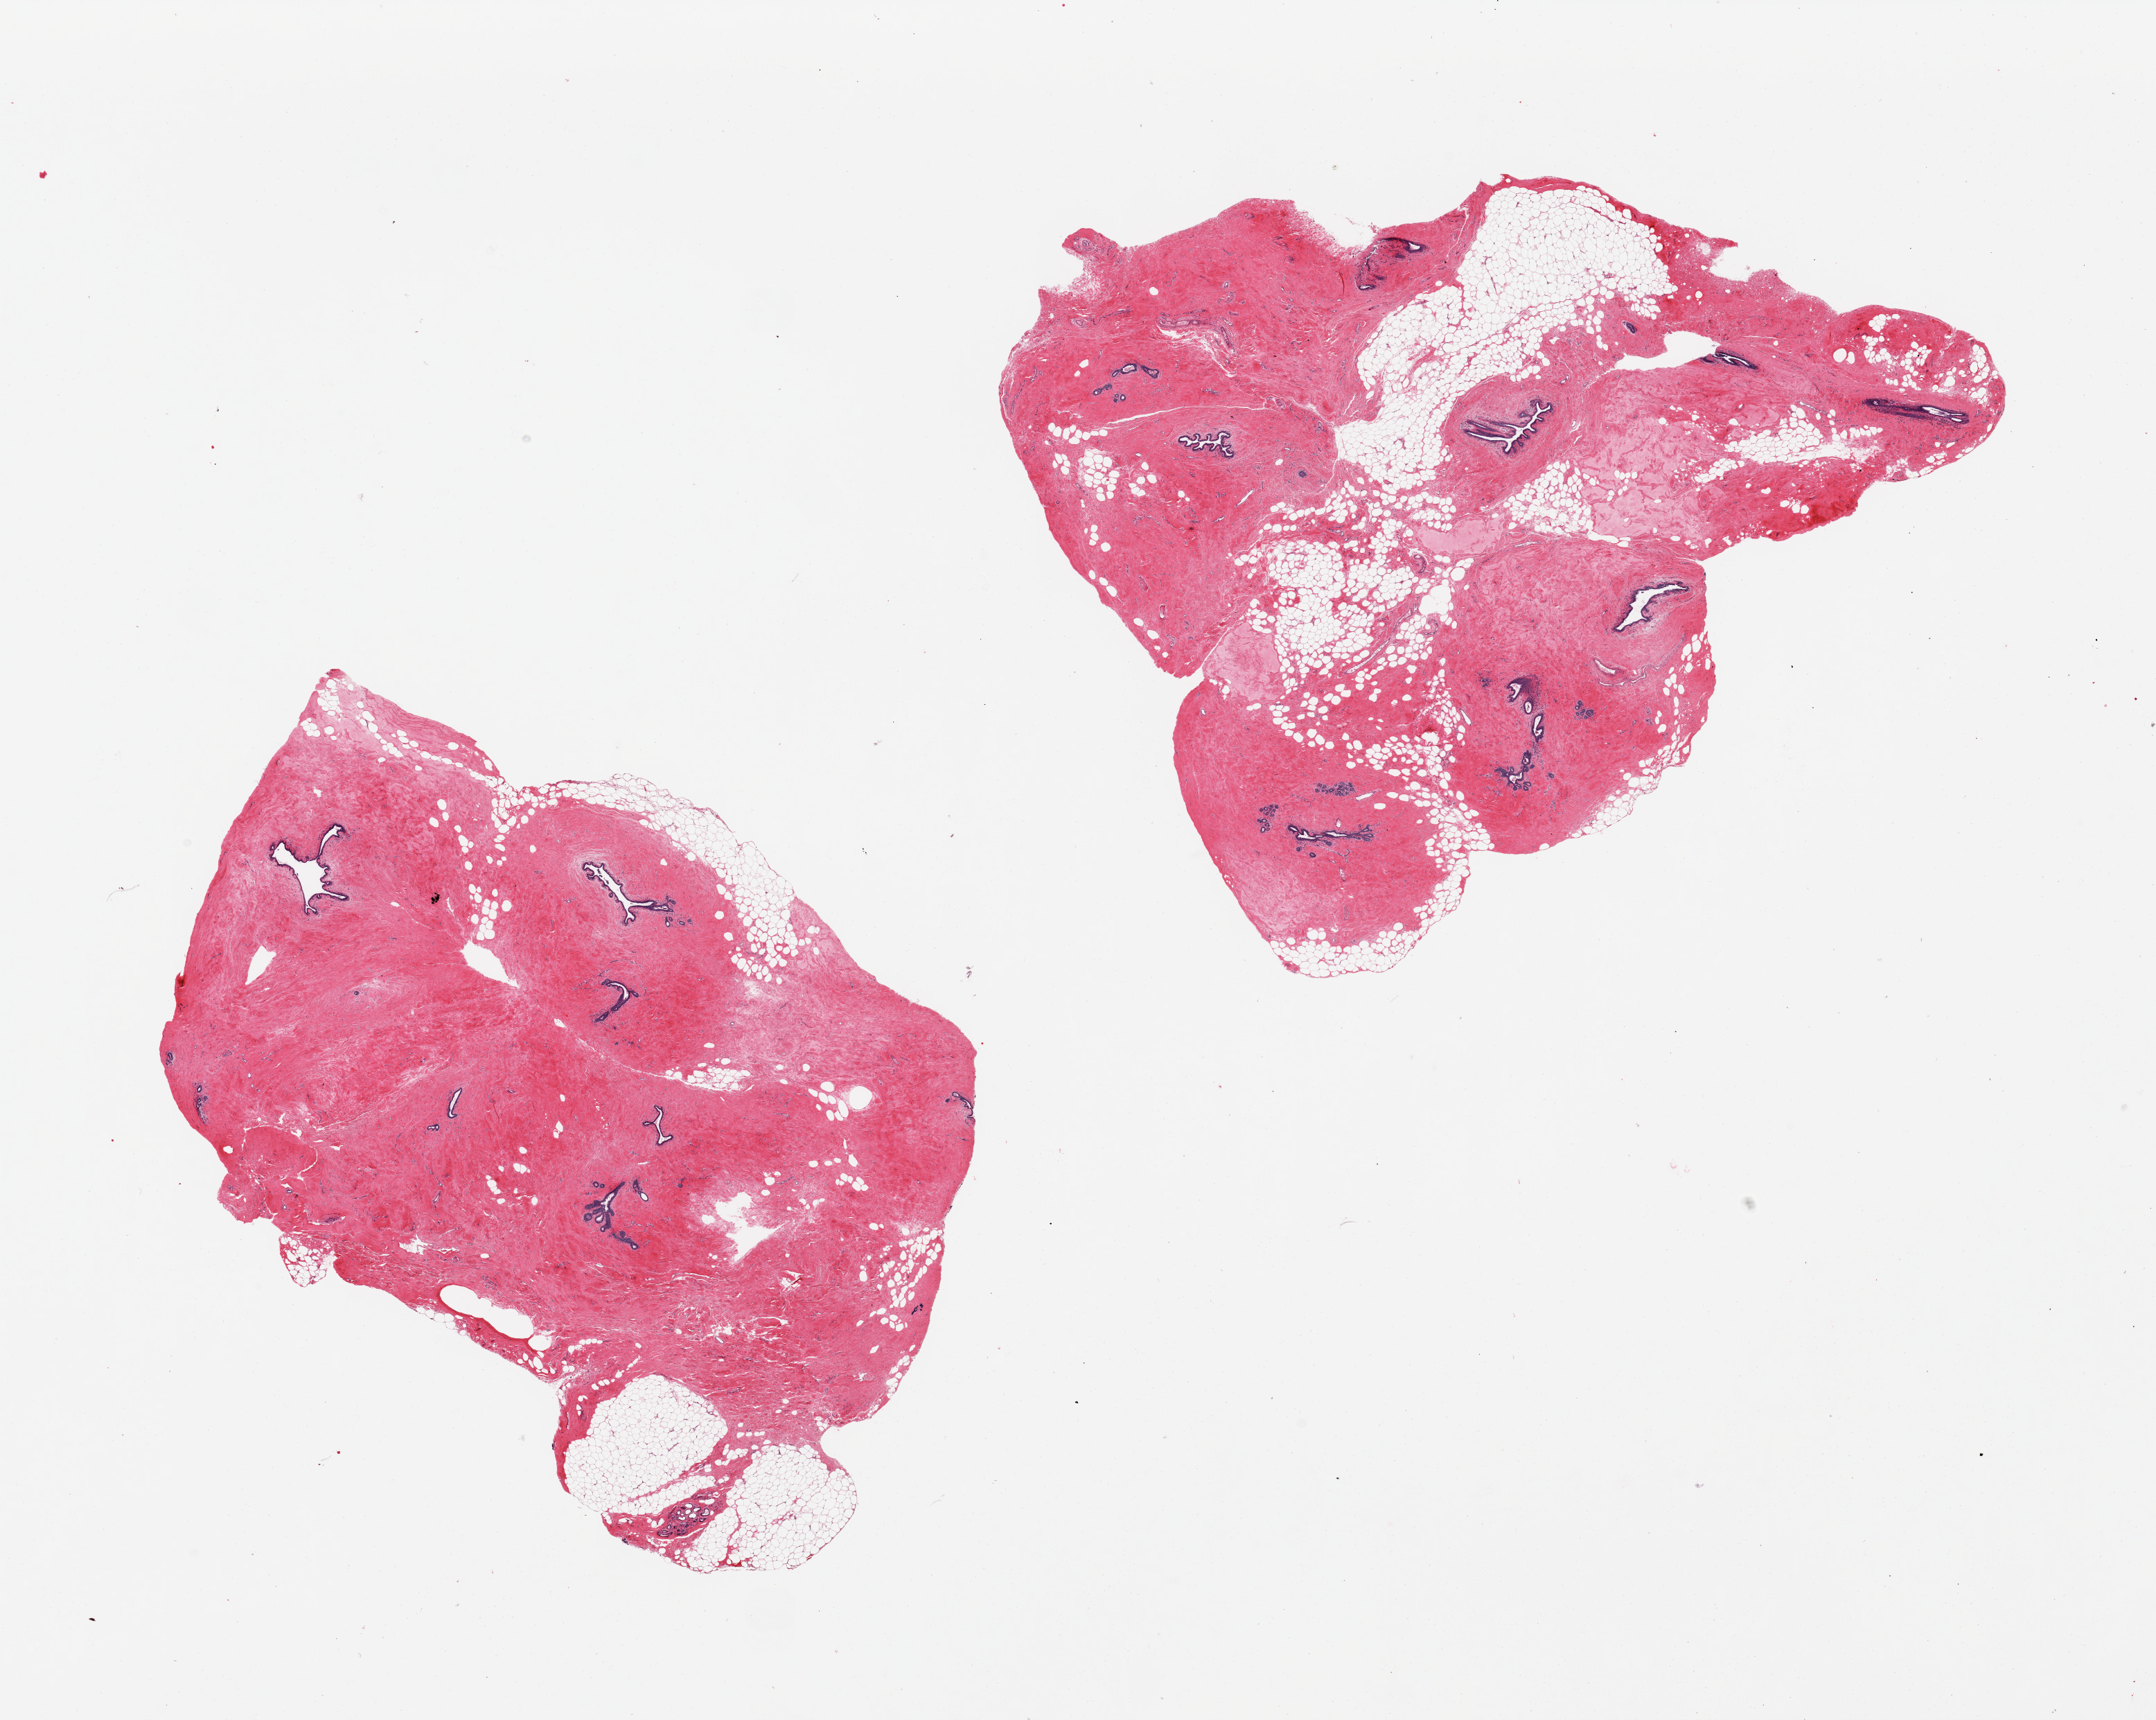
Whole-slide image, H&E stain — whole scanned area (about 24.6 x 19.6 mm, acquisition: 20x scan) shown as a low-resolution overview; PAXgene-fixed, paraffin-embedded tissue; section of breast (target tissue); donor tissue sample. Donor sex: female.
Pathologist's review note for this sample: 2 pieces, involuted TDLUs noted; Fibrocystic changes.